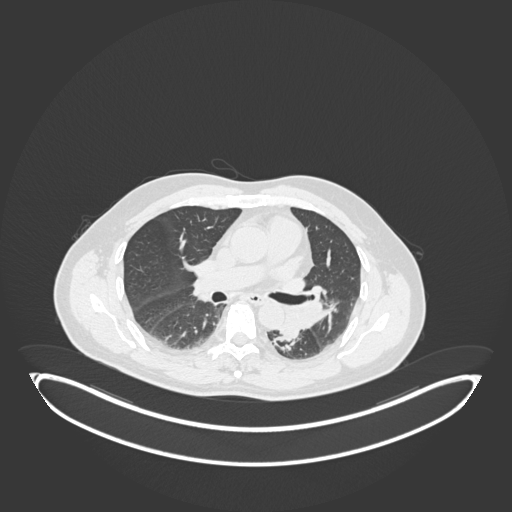
Chest CT, one axial slice. Position 115 of 258 along the scan axis. 120 kVp. Lung window (W 1500 / L -600 HU). 1 mm slice thickness. 512 × 512 image matrix, field of view 500 × 500 mm. Patient: male, 54 years. From the clinical record (not read from this slice): clinical TNM (as recorded): T3 N0 M0.
Outlined on this slice (rectangle marked by the reading radiologist):
- lung tumour (recorded histology: squamous cell carcinoma): bounding box (x1, y1, x2, y2) in pixels: (276, 304, 299, 346)